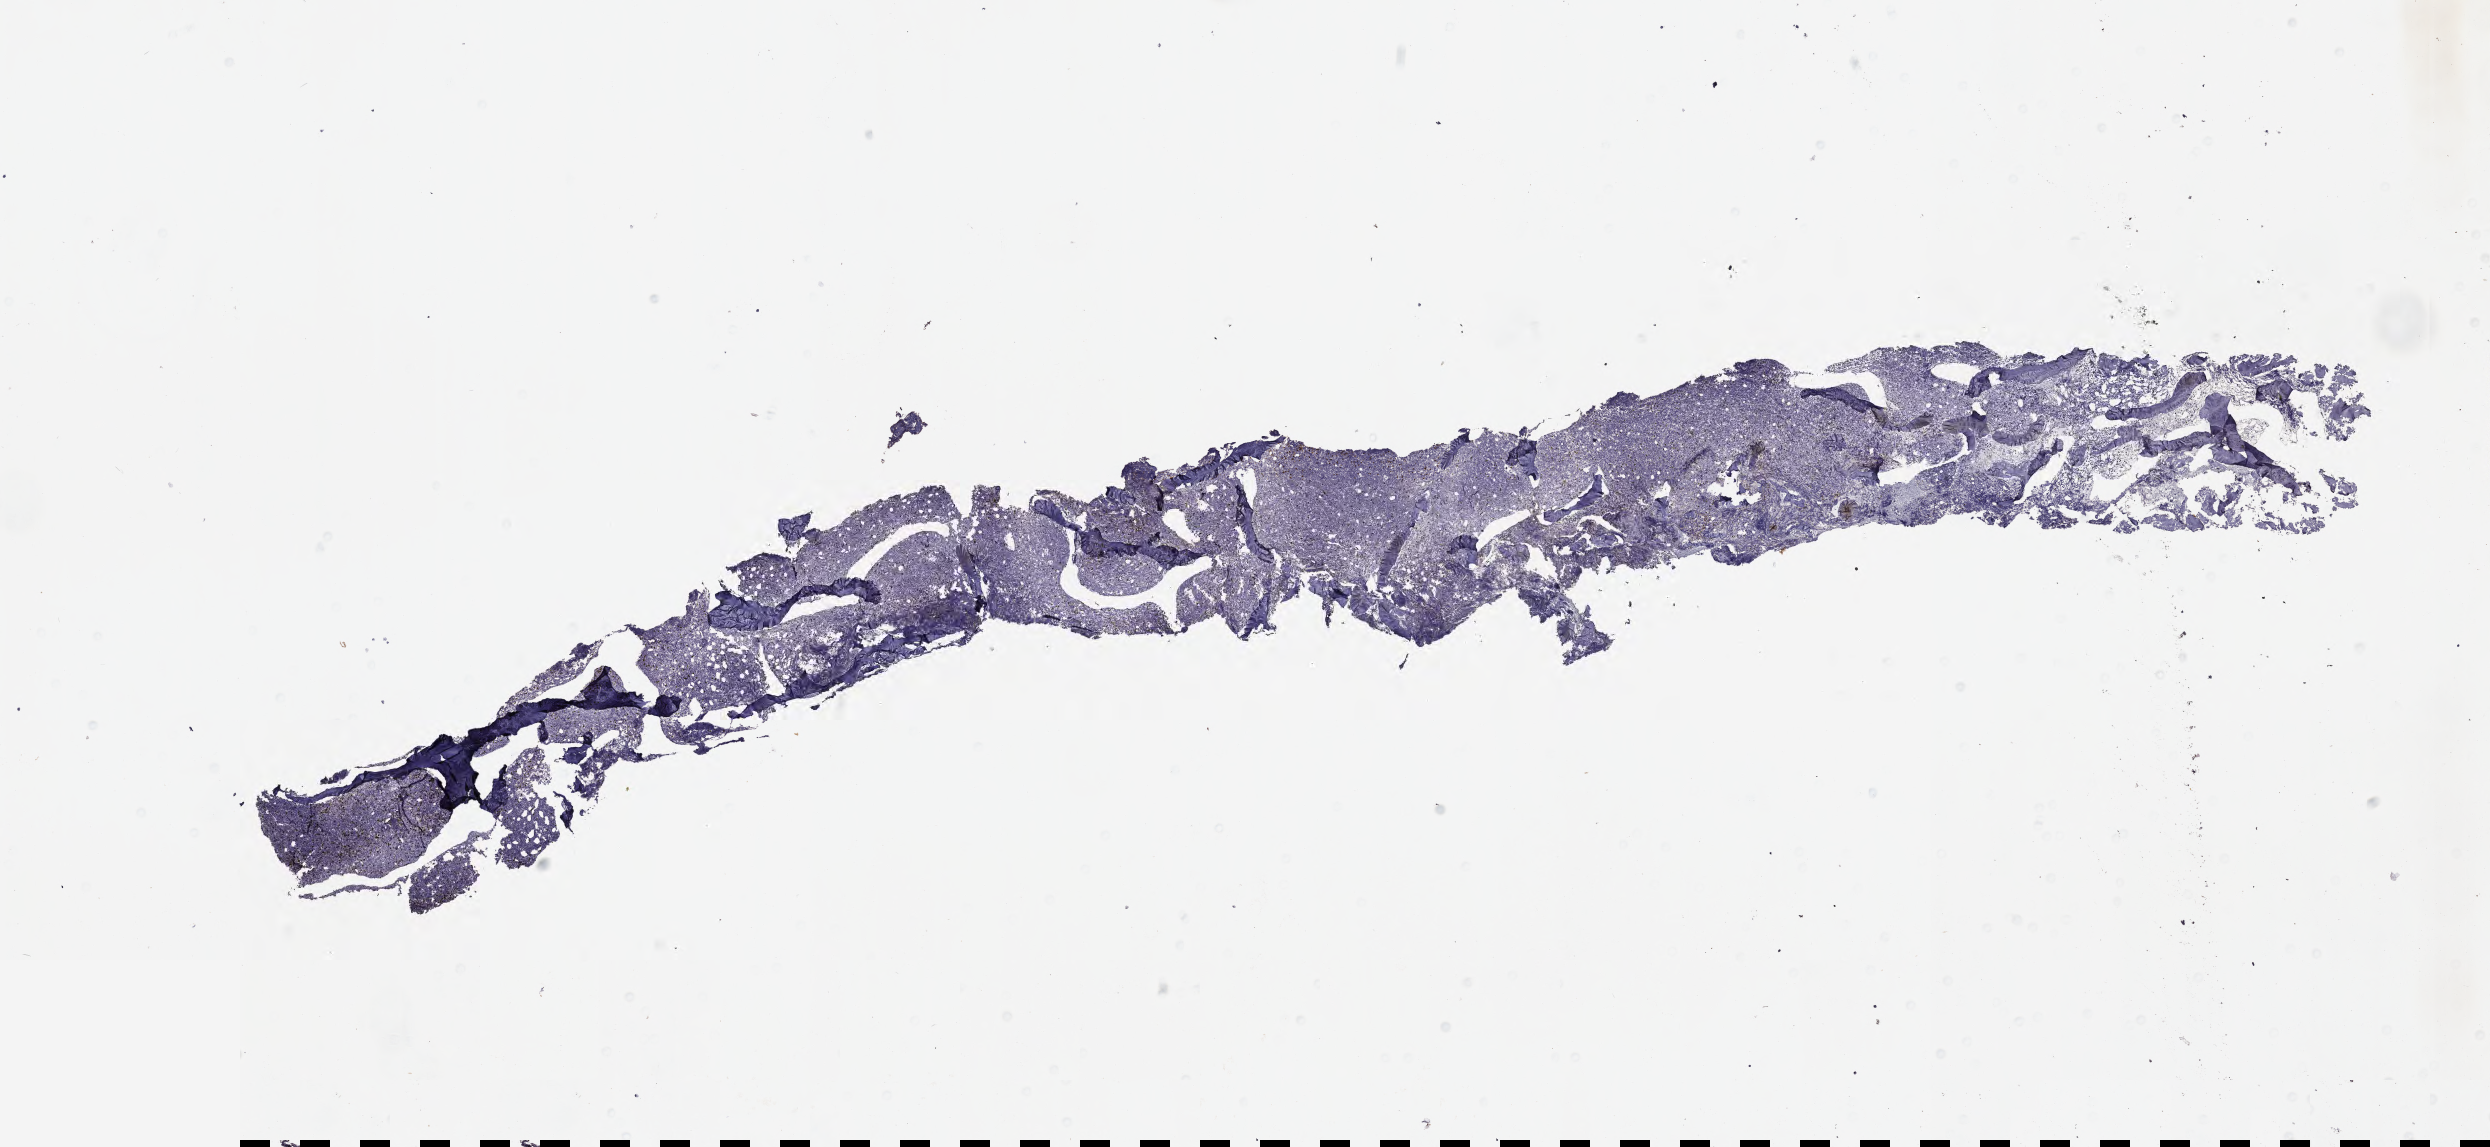
IHC for CD3, whole-slide image — shown as a low-resolution overview of the whole scanned area (about 20.1 x 9.3 mm); specimen: tumor tissue. Male patient.
* diagnosis: Burkitt lymphoma, NOS